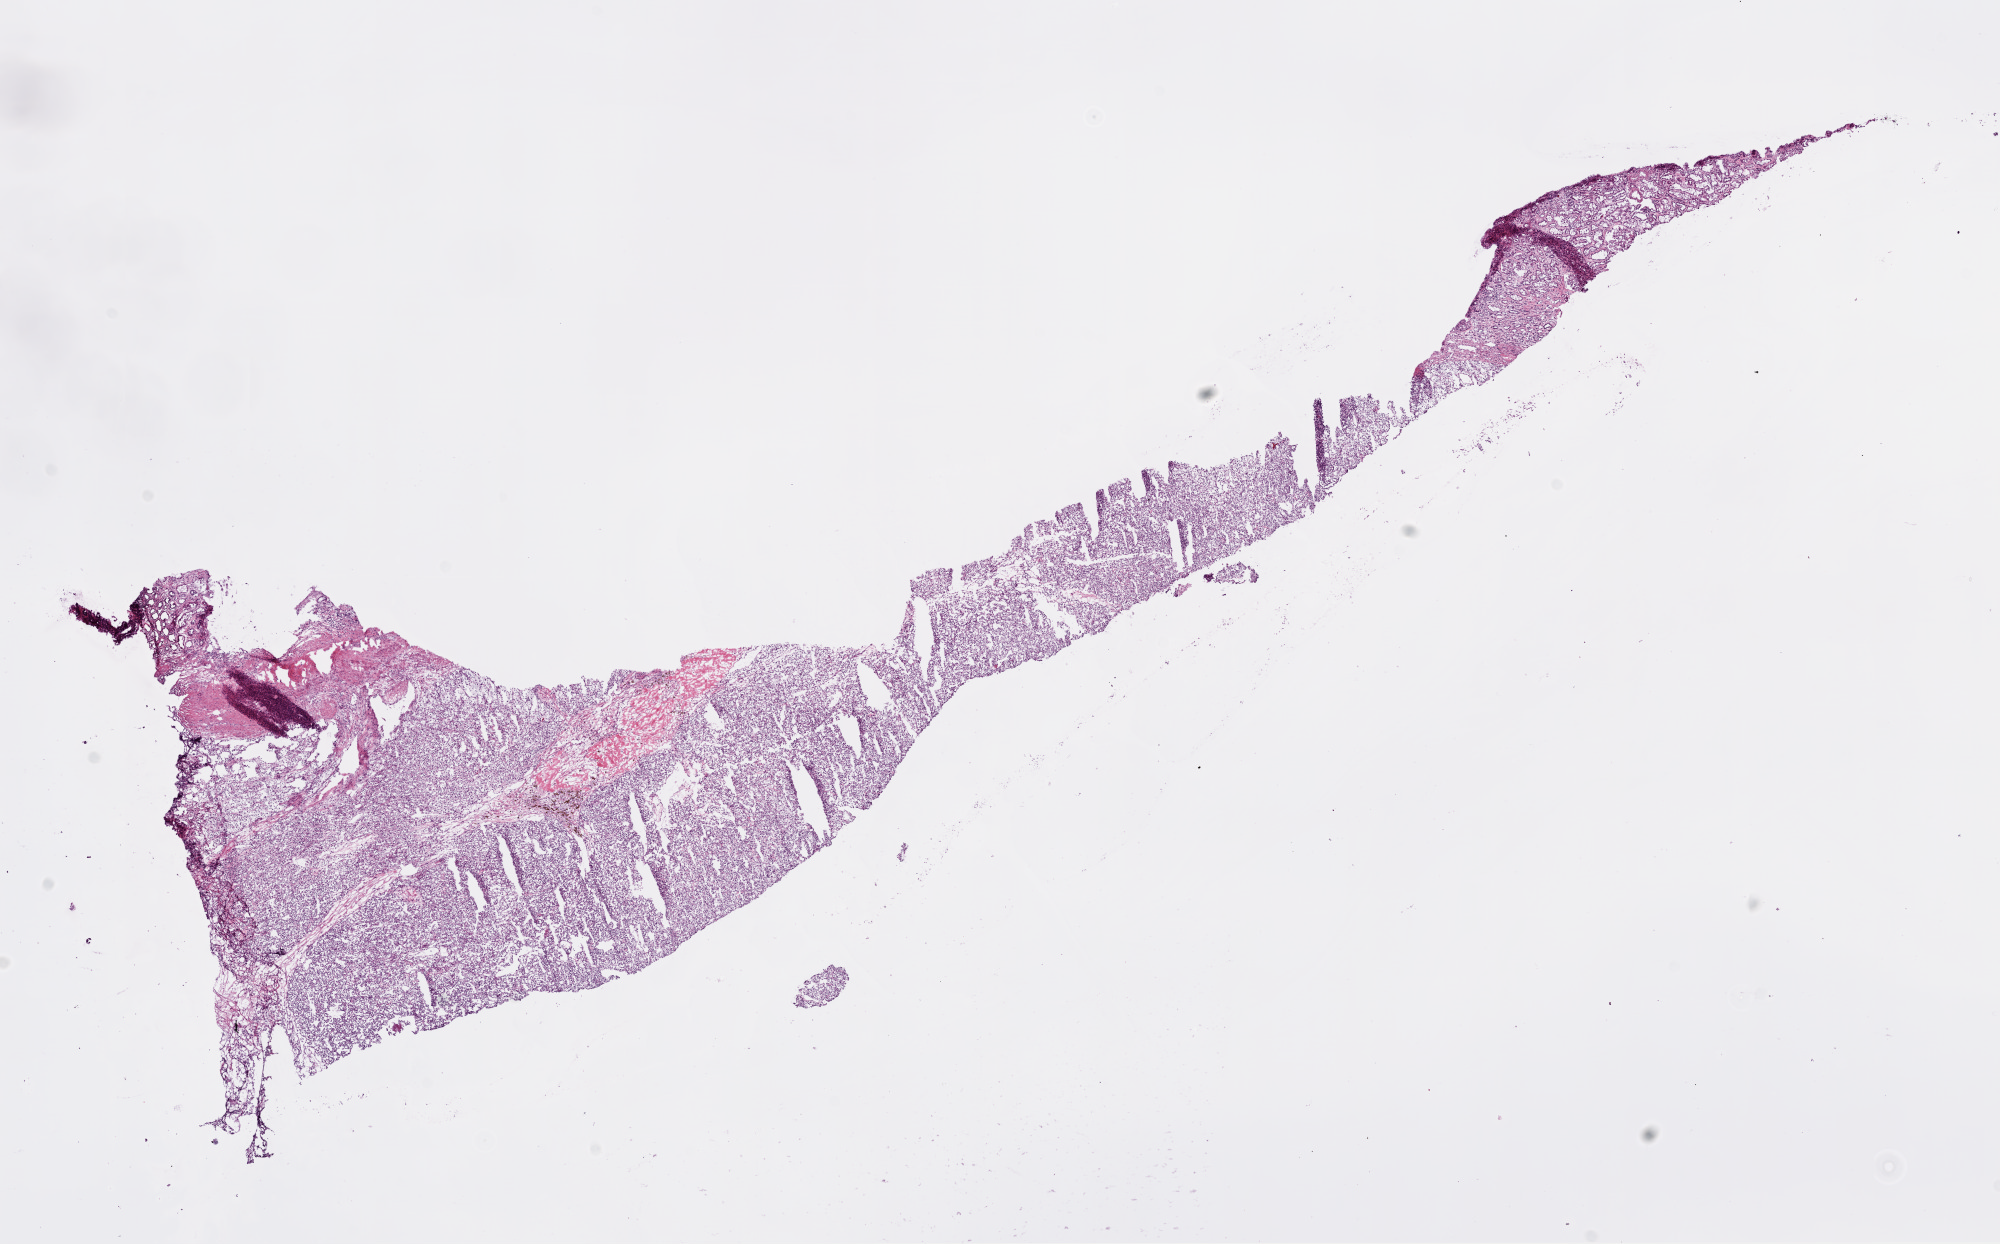
Digitized H&E tissue section (whole slide), shown as a low-resolution overview of the whole scanned area (about 16.0 x 10.0 mm). Frozen section from the bottom of the tissue portion. Kidney, primary tumour sample. Female, age 66 years at initial diagnosis. Histologic grade: G3 (poorly differentiated). Pathologist review of this section (percent, as recorded): tumour cells 75%, tumour nuclei 80%, normal cells 15%, stromal cells 10%, necrosis 0%.
AJCC pathologic stage: I. Diagnosis: Clear cell adenocarcinoma, NOS.